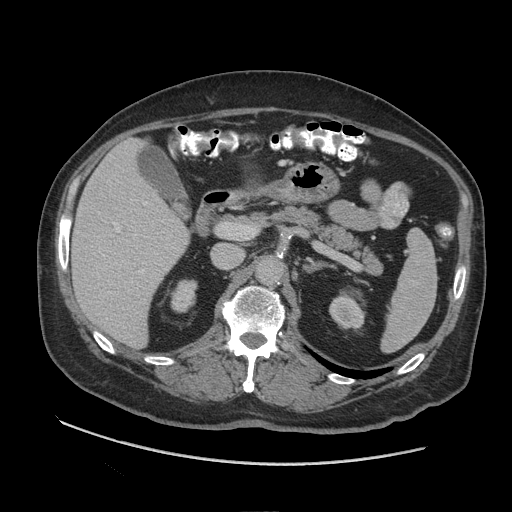
Contrast-enhanced abdominal CT (liver protocol), one axial slice; position 50 of 109 along the scan axis; reconstruction kernel STANDARD; 140 kVp; soft-tissue window (W 400 / L 40 HU); 2.5 mm slice thickness; 512 × 512 image matrix, field of view 420 × 420 mm. From the clinical record (not read from this slice): diagnosis: hepatocellular carcinoma (patient treated with transarterial chemoembolisation; whether this scan precedes or follows treatment is not stated here); TNM stage (as recorded): Stage-I; Child-Pugh class: A.
Structures marked on this image (semi-automatically segmented with operator editing):
- liver parenchyma outside the tumour (the mass and vessels are separate outlines, so this box may not span the whole liver): bounding box (x1, y1, x2, y2) in pixels: (70, 138, 188, 346)
- liver vessels: (93, 202, 164, 273)